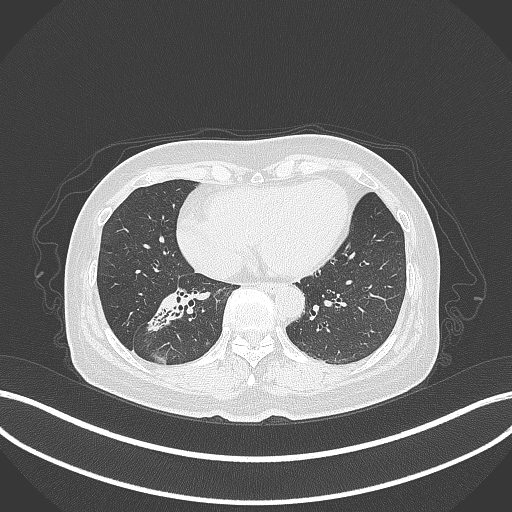
Chest CT, one axial slice. Position 140 of 429 along the scan axis. Reconstruction kernel B70f. Lung window (W 1500 / L -600 HU). 1 mm slice thickness. 512 × 512 image matrix, field of view 400 × 400 mm. Patient: female, 67 years. Case-level facts recorded for this patient, not image findings: clinical TNM (as recorded): T1c N1 M0; histopathological grade: G2-3.
Structures marked on this image (rectangle marked by the reading radiologist):
- lung tumour (recorded histology: adenocarcinoma): bounding box <142,289,196,334> (left, top, right, bottom; pixels)